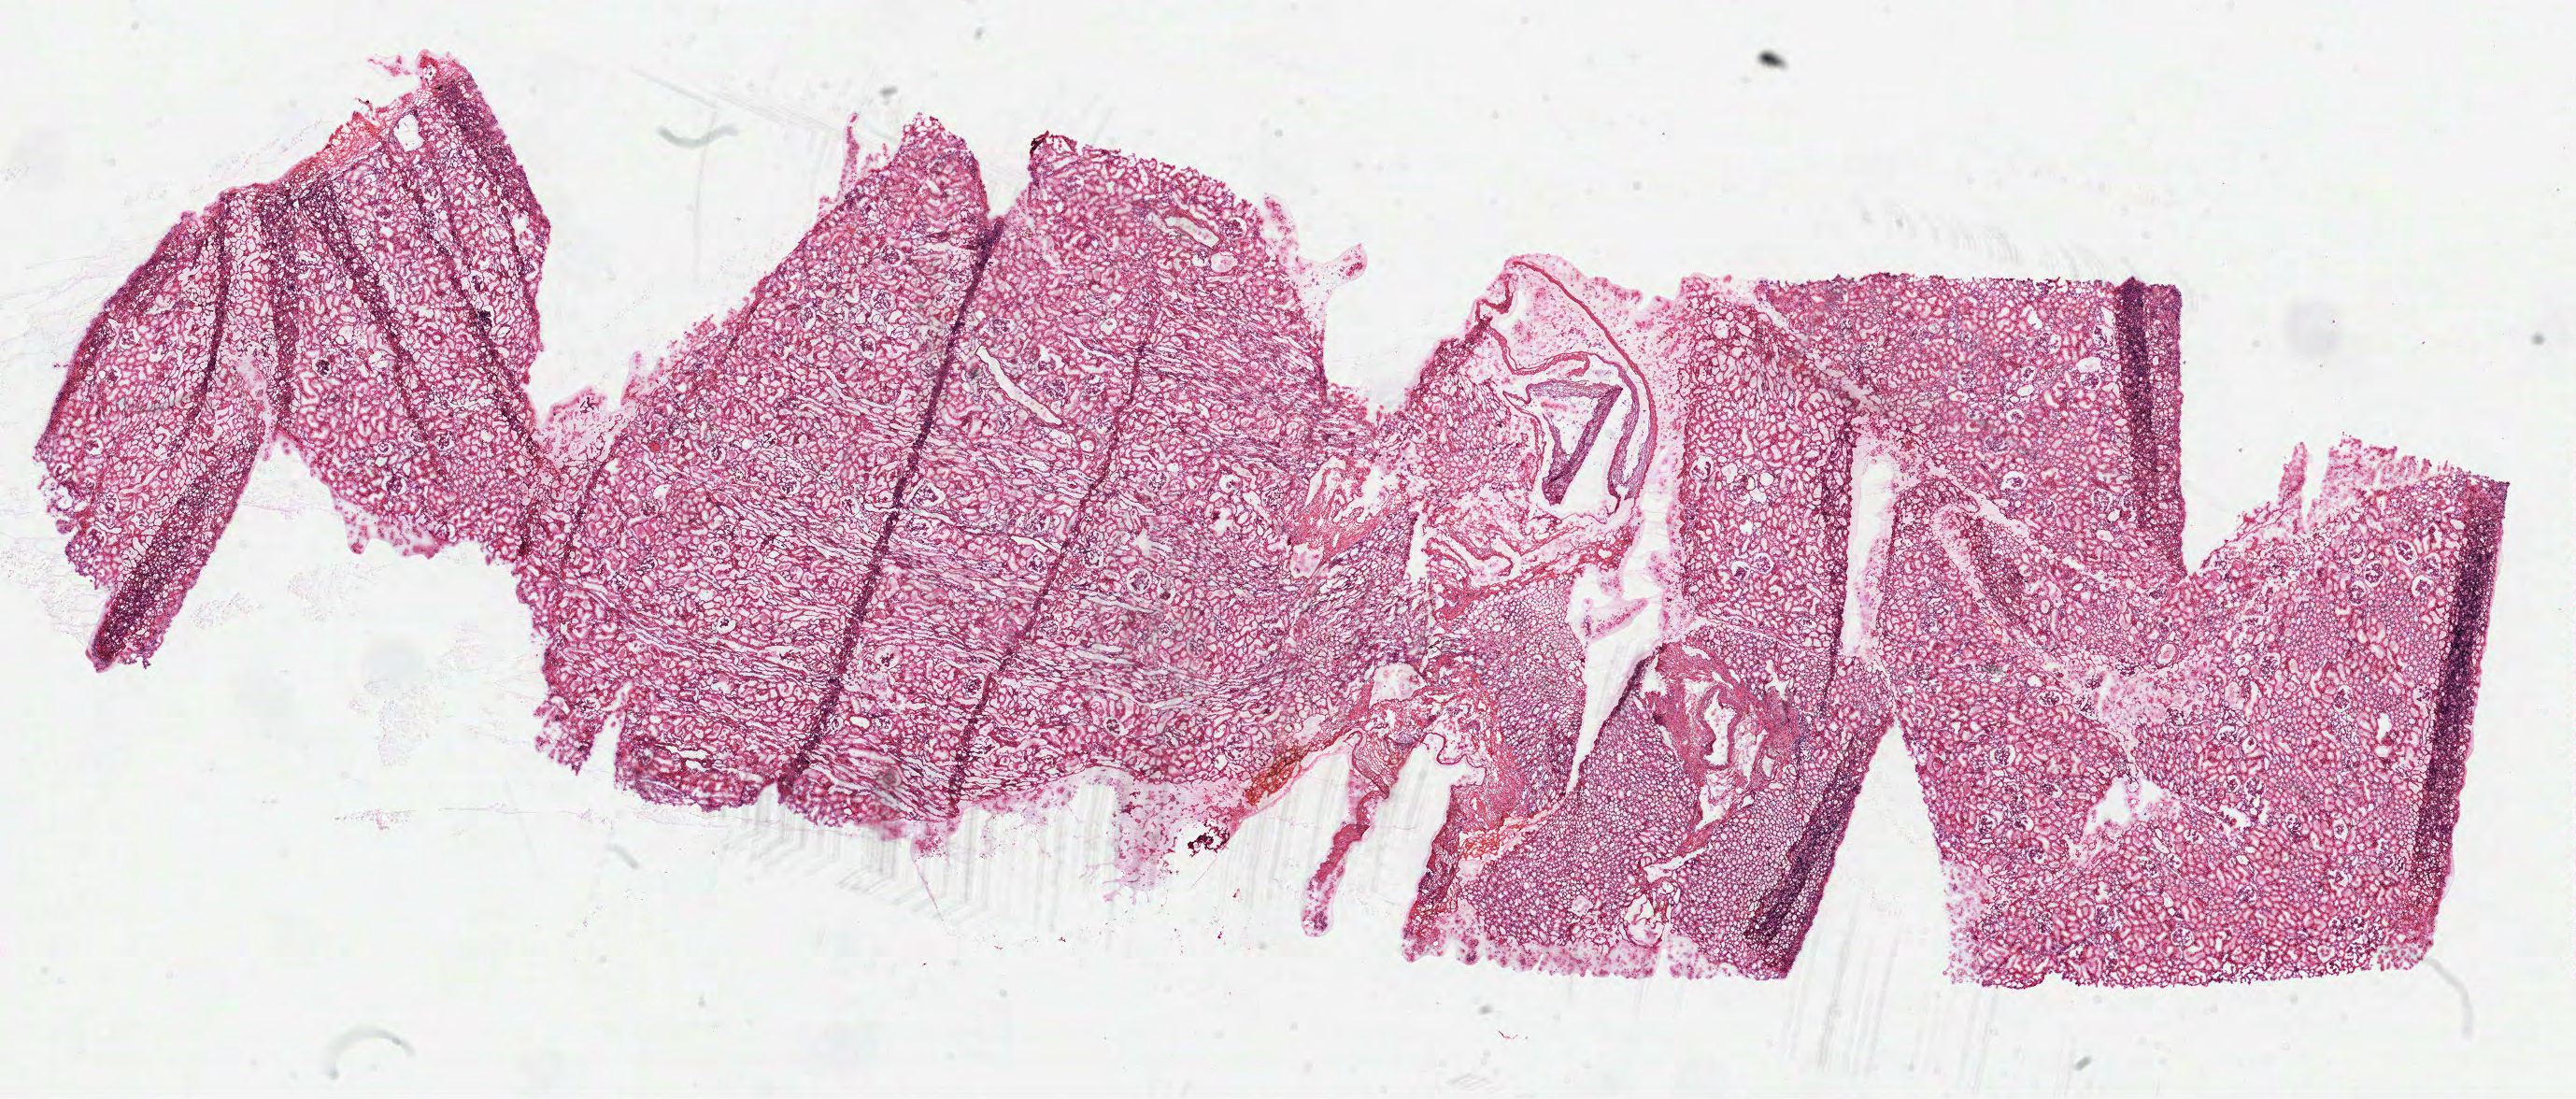
Whole-slide histology image, H&E-stained — low-resolution overview of the scanned area, about 22.2 x 9.5 mm (acquisition: 40x scan); frozen section from the top of the tissue portion; kidney, solid tissue normal (non-tumour tissue) sample. Female, age 63 years at initial diagnosis.
* this section: solid tissue normal (non-tumour) sample from the same patient
* patient diagnosis: Clear cell adenocarcinoma, NOS